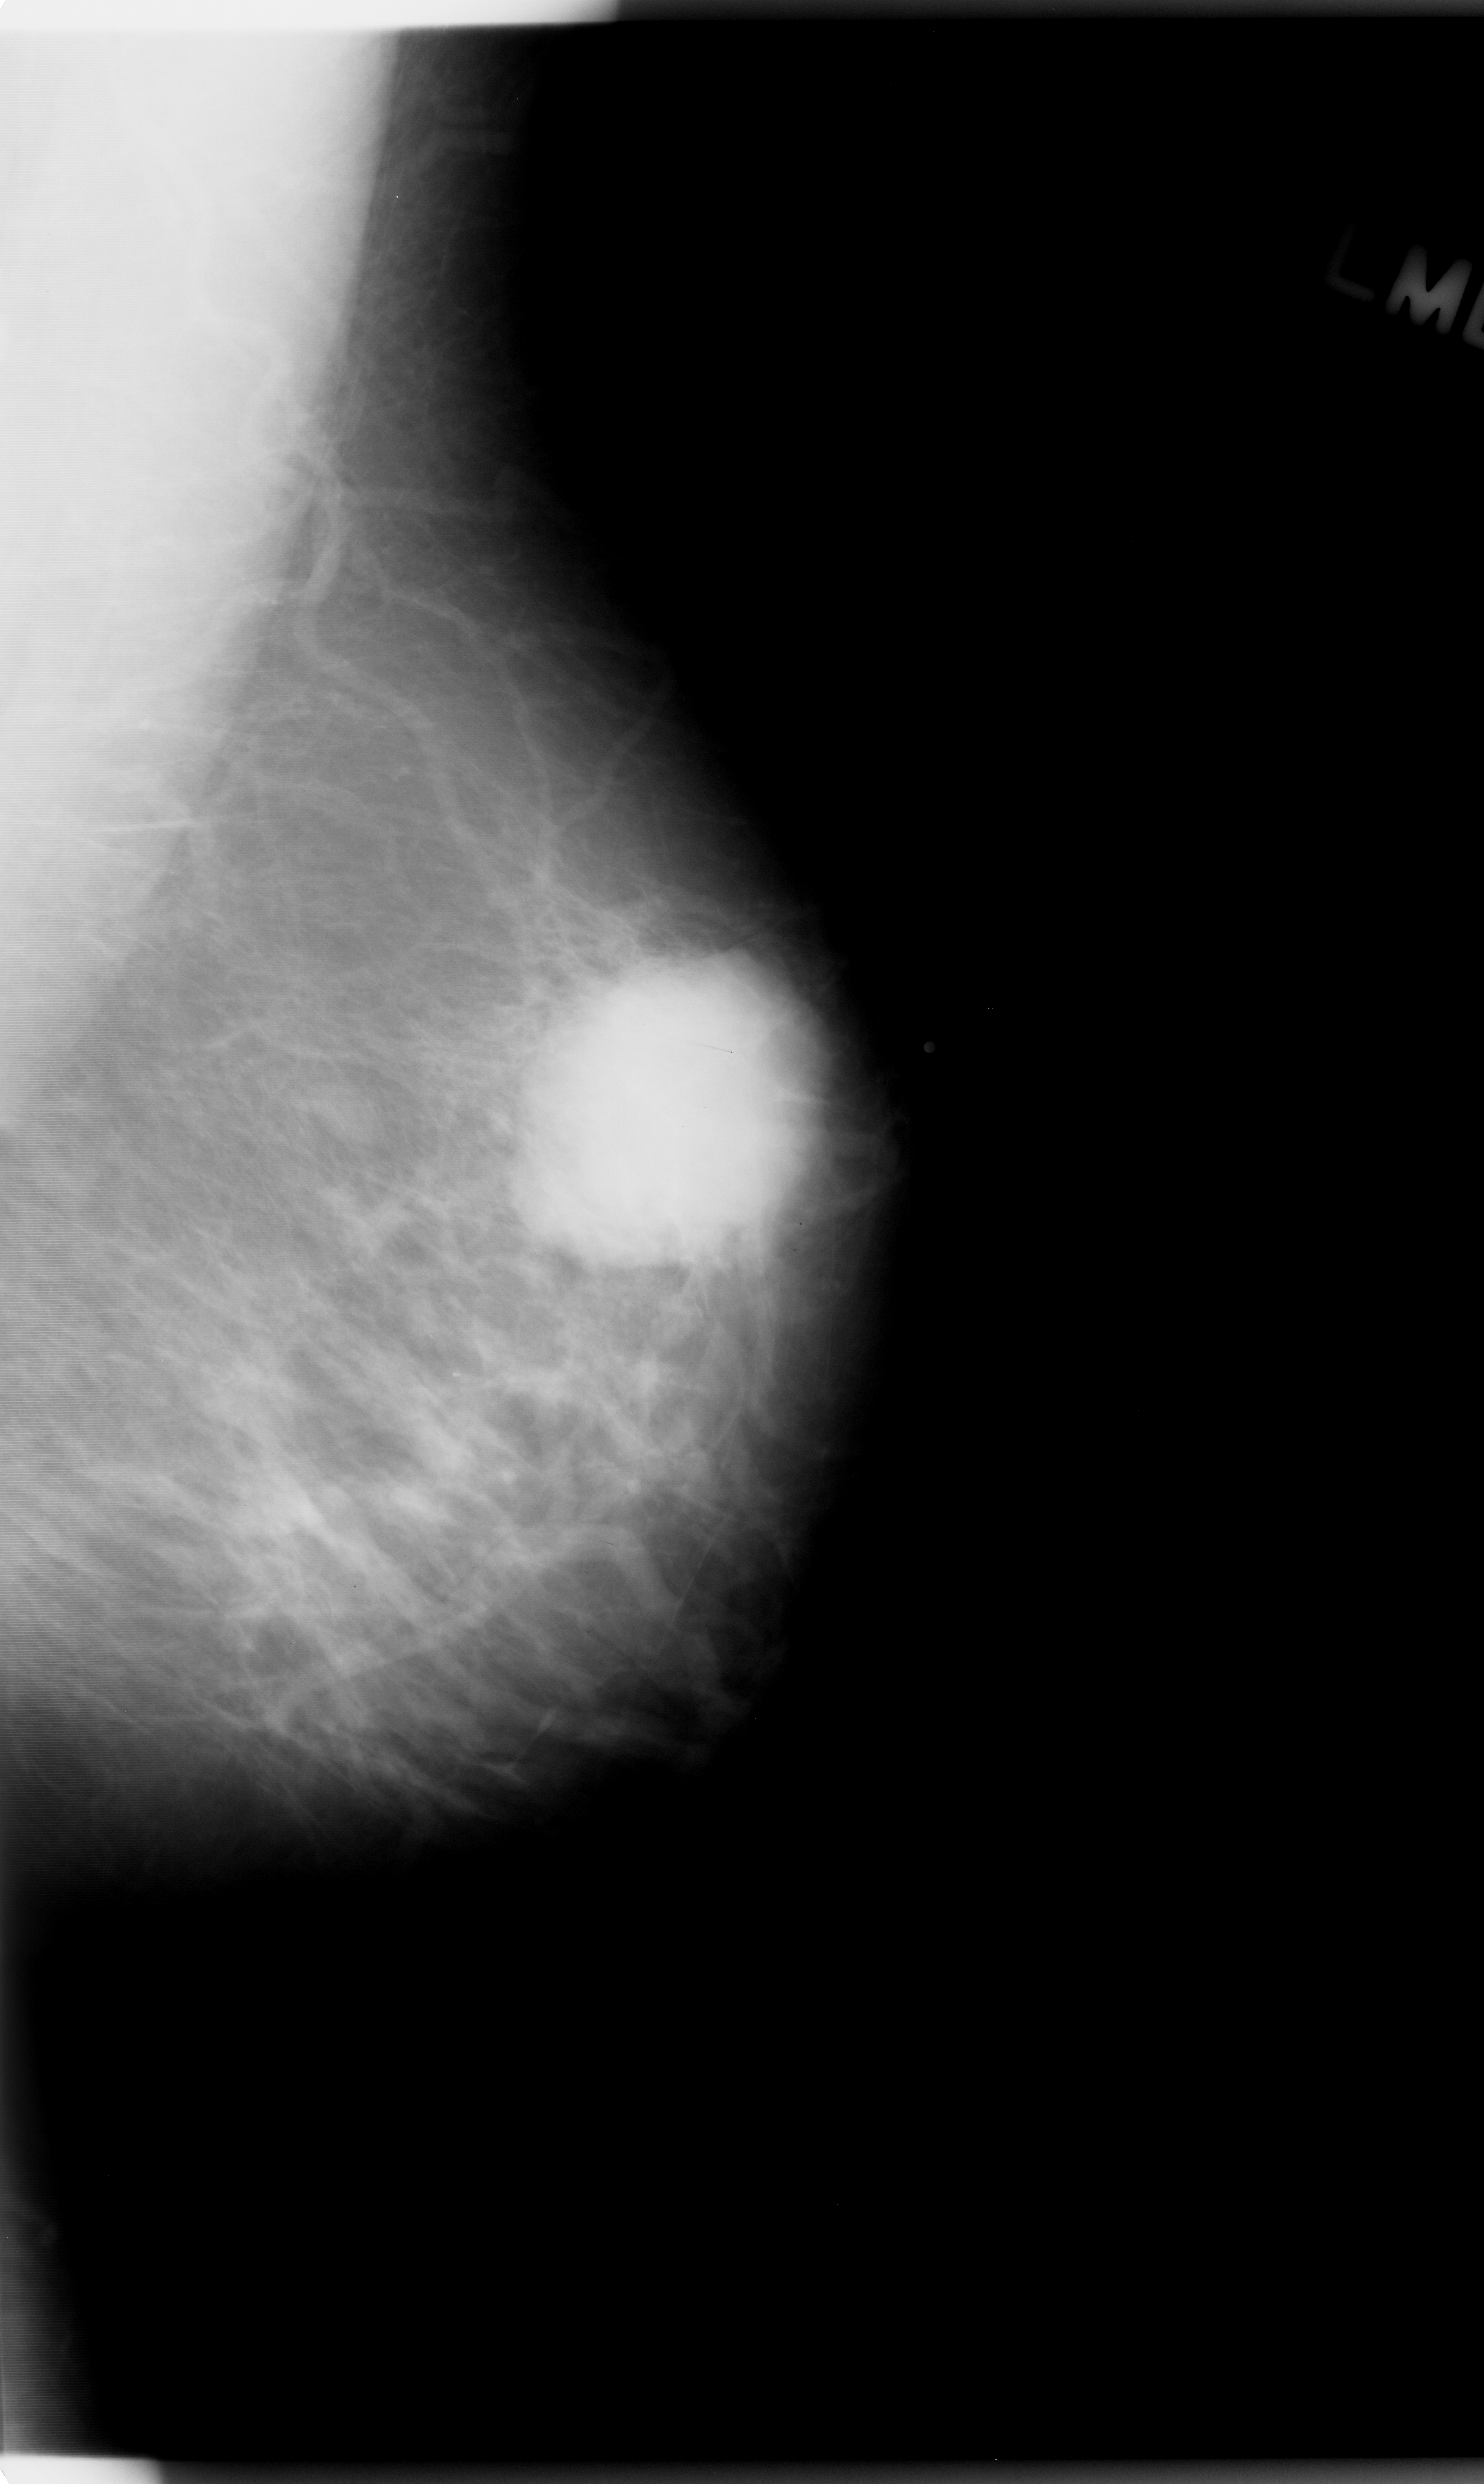
Mammogram (digitized film); left breast; mediolateral oblique (MLO) view; BI-RADS breast density category 2 (scale 1–4); 1484 × 2484 image matrix.
Expert-marked regions of interest on this image (one box per marked abnormality):
- mass, shape oval, margins microlobulated; BI-RADS assessment category 5; subtlety rating 5 on a 1 (subtle) to 5 (obvious) scale; pathology result (as recorded, not read from the image): malignant: bounding box [x1, y1, x2, y2] px = [511, 944, 854, 1247]